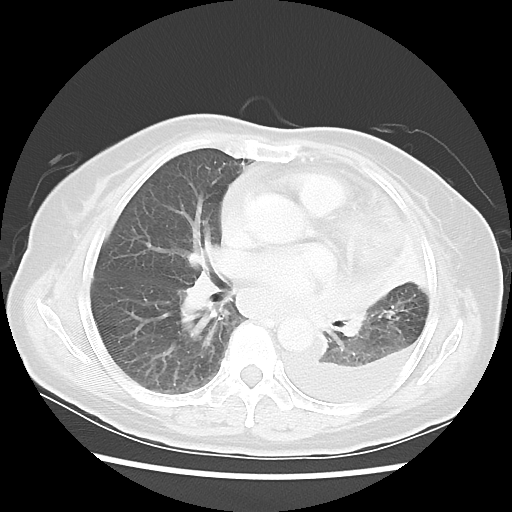
Chest CT, one axial slice. Lung window (W 1500 / L -600 HU). 5 mm slice thickness. 512 × 512 image matrix, field of view 336 × 336 mm. Female patient, age 72 years. Case-level facts recorded for this patient, not image findings: clinical TNM (as recorded): T4 N3 M1b; histopathological grade: G3.
Outlined on this slice (rectangle marked by the reading radiologist):
- lung tumour (recorded histology: large cell carcinoma): bounding box (x1, y1, x2, y2) in pixels: (295, 271, 392, 359)